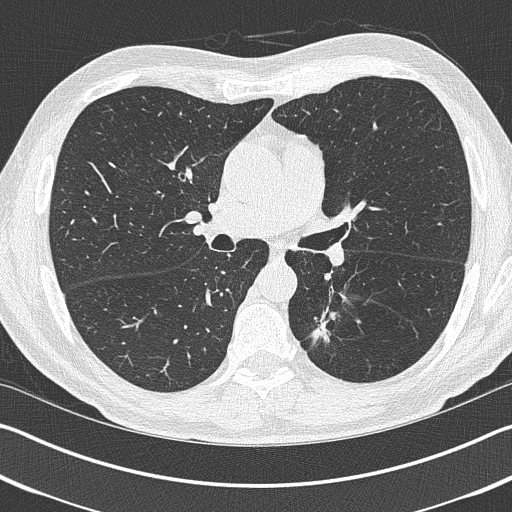
Low-dose screening chest CT, axial slice; first (baseline) screen; lung window (W 1500 / L -600 HU); 1 mm slice thickness; lung (sharp) reconstruction kernel (B50f); slice 163 of 402 in the series; 512 × 512 image matrix, field of view 340 × 340 mm. Male, age 69 years at enrolment.
- Expert reader's lesion annotation, bounding box <299,308,354,361> (left, top, right, bottom; pixels).
- Screening reader's record for this exam (one nodule recorded; not confirmed to be the boxed lesion): non-calcified nodule or mass ≥4 mm, left upper lobe, 19 × 19 mm, spiculated (stellate) margins, pre-existing on the prior screen: yes.